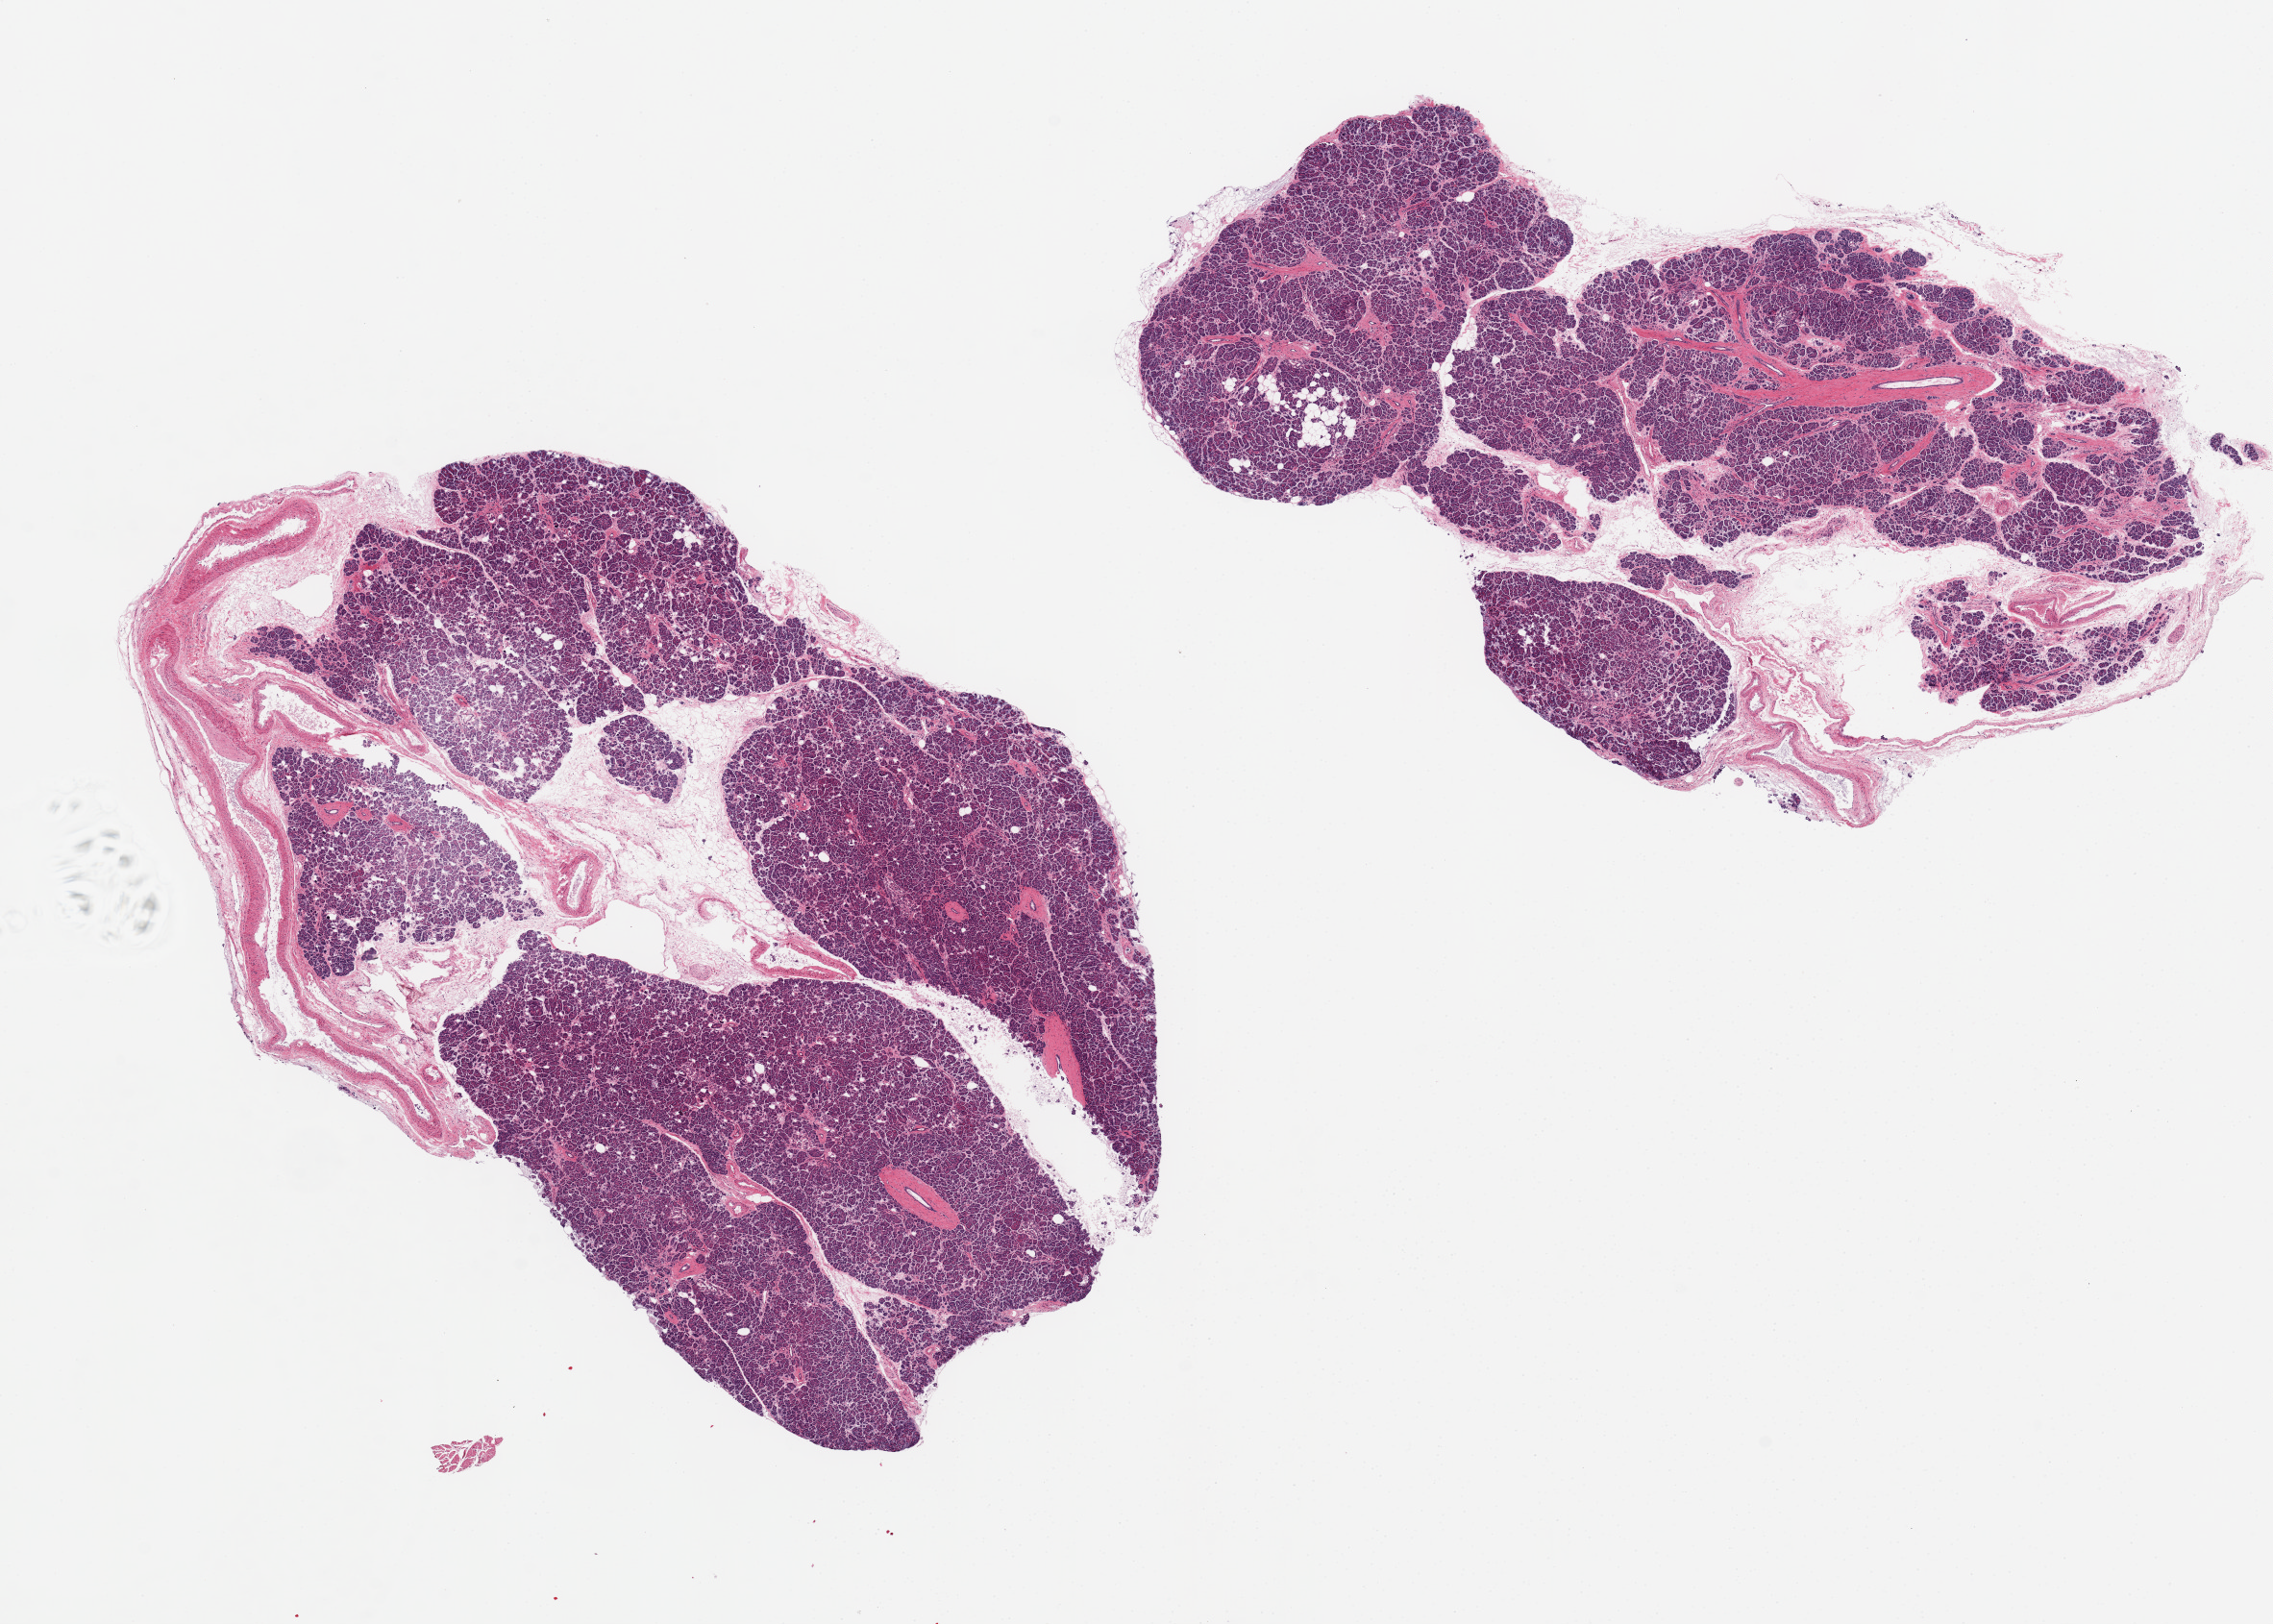
Hematoxylin and eosin (H&E) whole-slide image, brightfield, shown as a low-resolution overview of the whole scanned area (about 18.7 x 13.4 mm, slide scanned at 20x). PAXgene-fixed paraffin-embedded (PFPE) section. Sampled site (target tissue): pancreas. Donor tissue sample. Donor: male.
Pathologist's review note for this sample: 2 pieces 9x6 & 9x5 mm; 20% adipose.